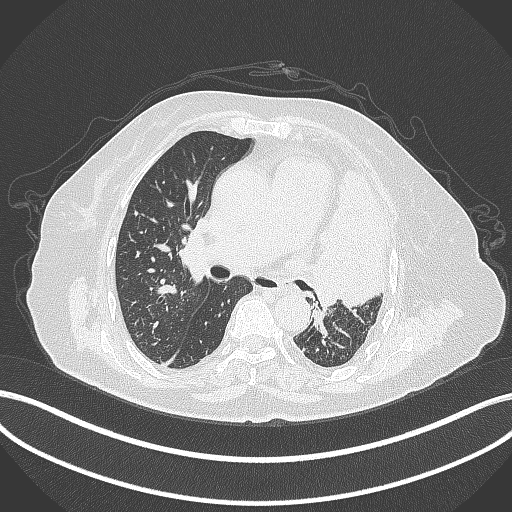
Chest CT, one axial slice. Position 219 of 399 along the scan axis. Reconstruction kernel B70f. 120 kVp. Lung window (W 1500 / L -600 HU). 1 mm slice thickness. 512 × 512 image matrix, field of view 400 × 400 mm. Patient: female, 75 years. From the clinical record (not read from this slice): clinical TNM (as recorded): T3 N3 M1.
Outlined on this slice (rectangle marked by the reading radiologist):
- lung tumour (recorded histology: adenocarcinoma): bounding box <304,167,391,312> (left, top, right, bottom; pixels)